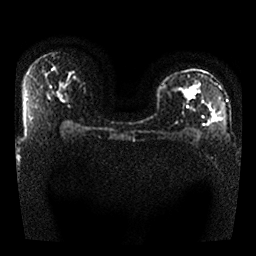
Breast MRI, one axial slice; slice 17 of 25 in the series (ordered by position); diffusion-weighted series; image 2 of 4 stored at this slice position (different b-values; order by instance number); 1.5 T; 4 mm slice thickness; 256 × 256 image matrix, field of view 330 × 330 mm. Female patient.
Structures marked on this image (manually delineated by an expert):
- tumour on diffusion-weighted imaging: bounding box [x1, y1, x2, y2] px = [184, 88, 221, 122]